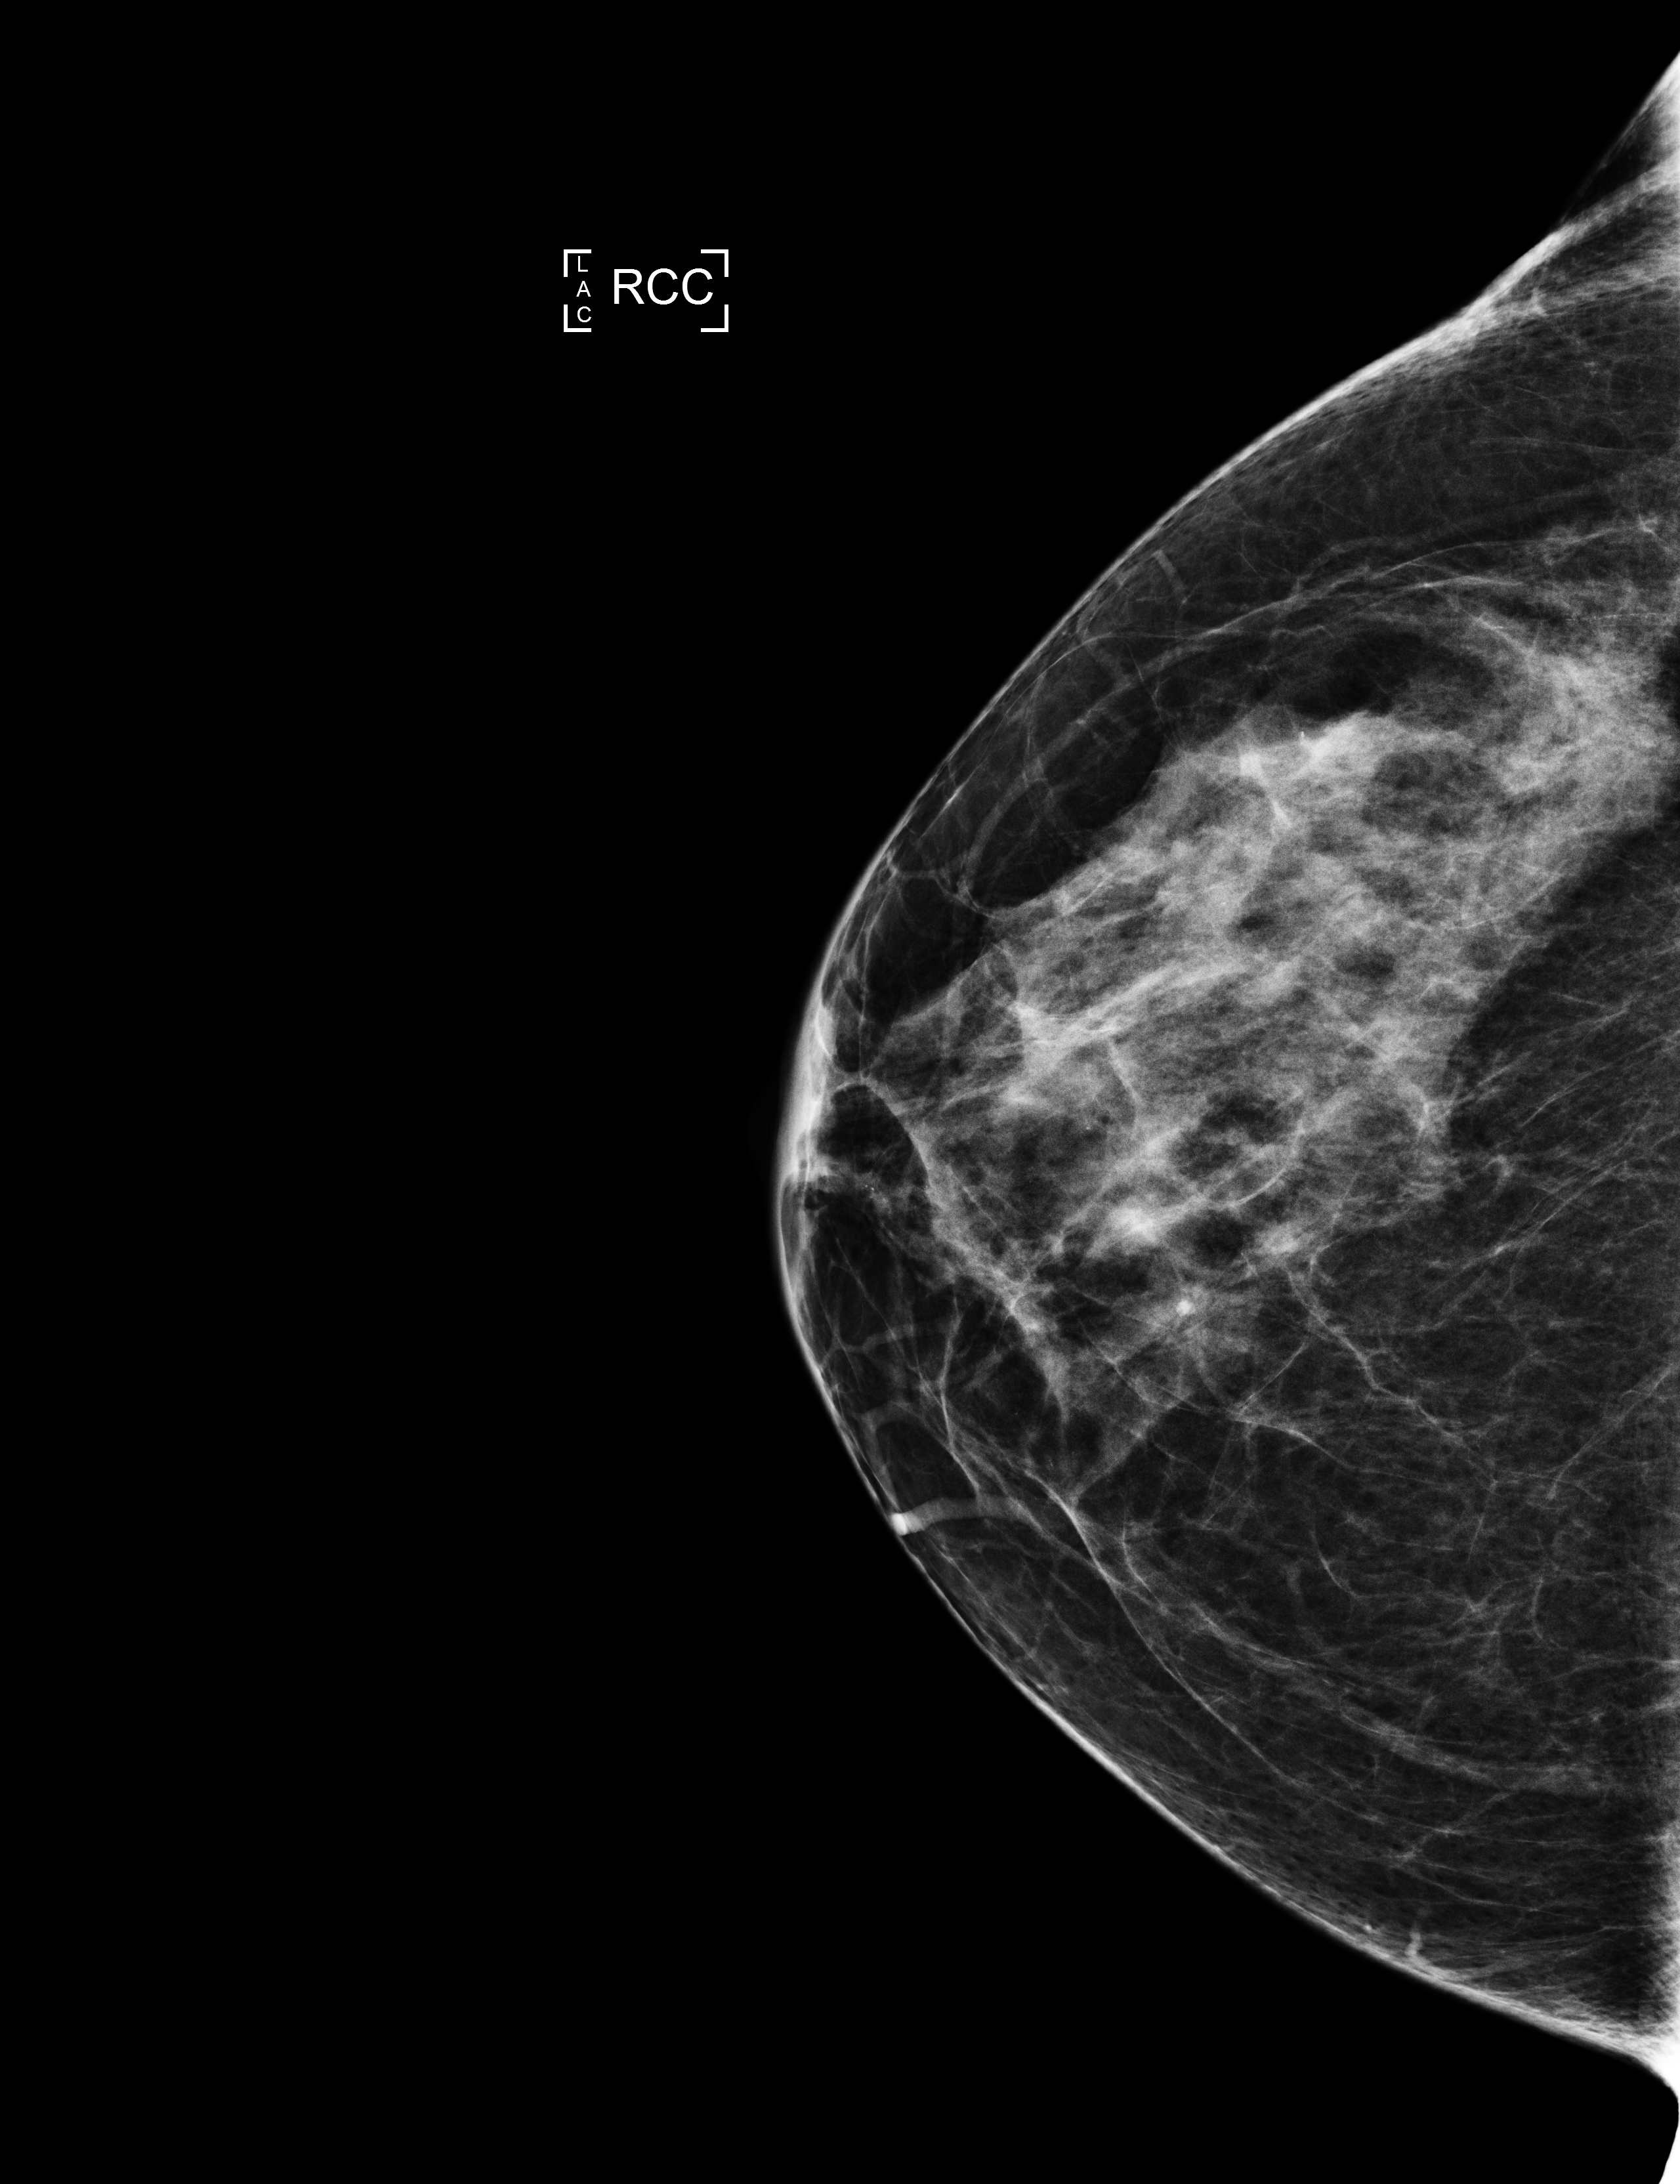
Full-field digital mammogram (FFDM), right breast, CC view, screening examination, compressed breast thickness 62 mm. Patient aged 63 years (female).
BI-RADS breast density category at the screening exam (both breasts, scale 1–4): 3. Final BI-RADS assessment for this screening round (tomosynthesis exam, both breasts): category 1. Recall: recalled for additional imaging after this screen.